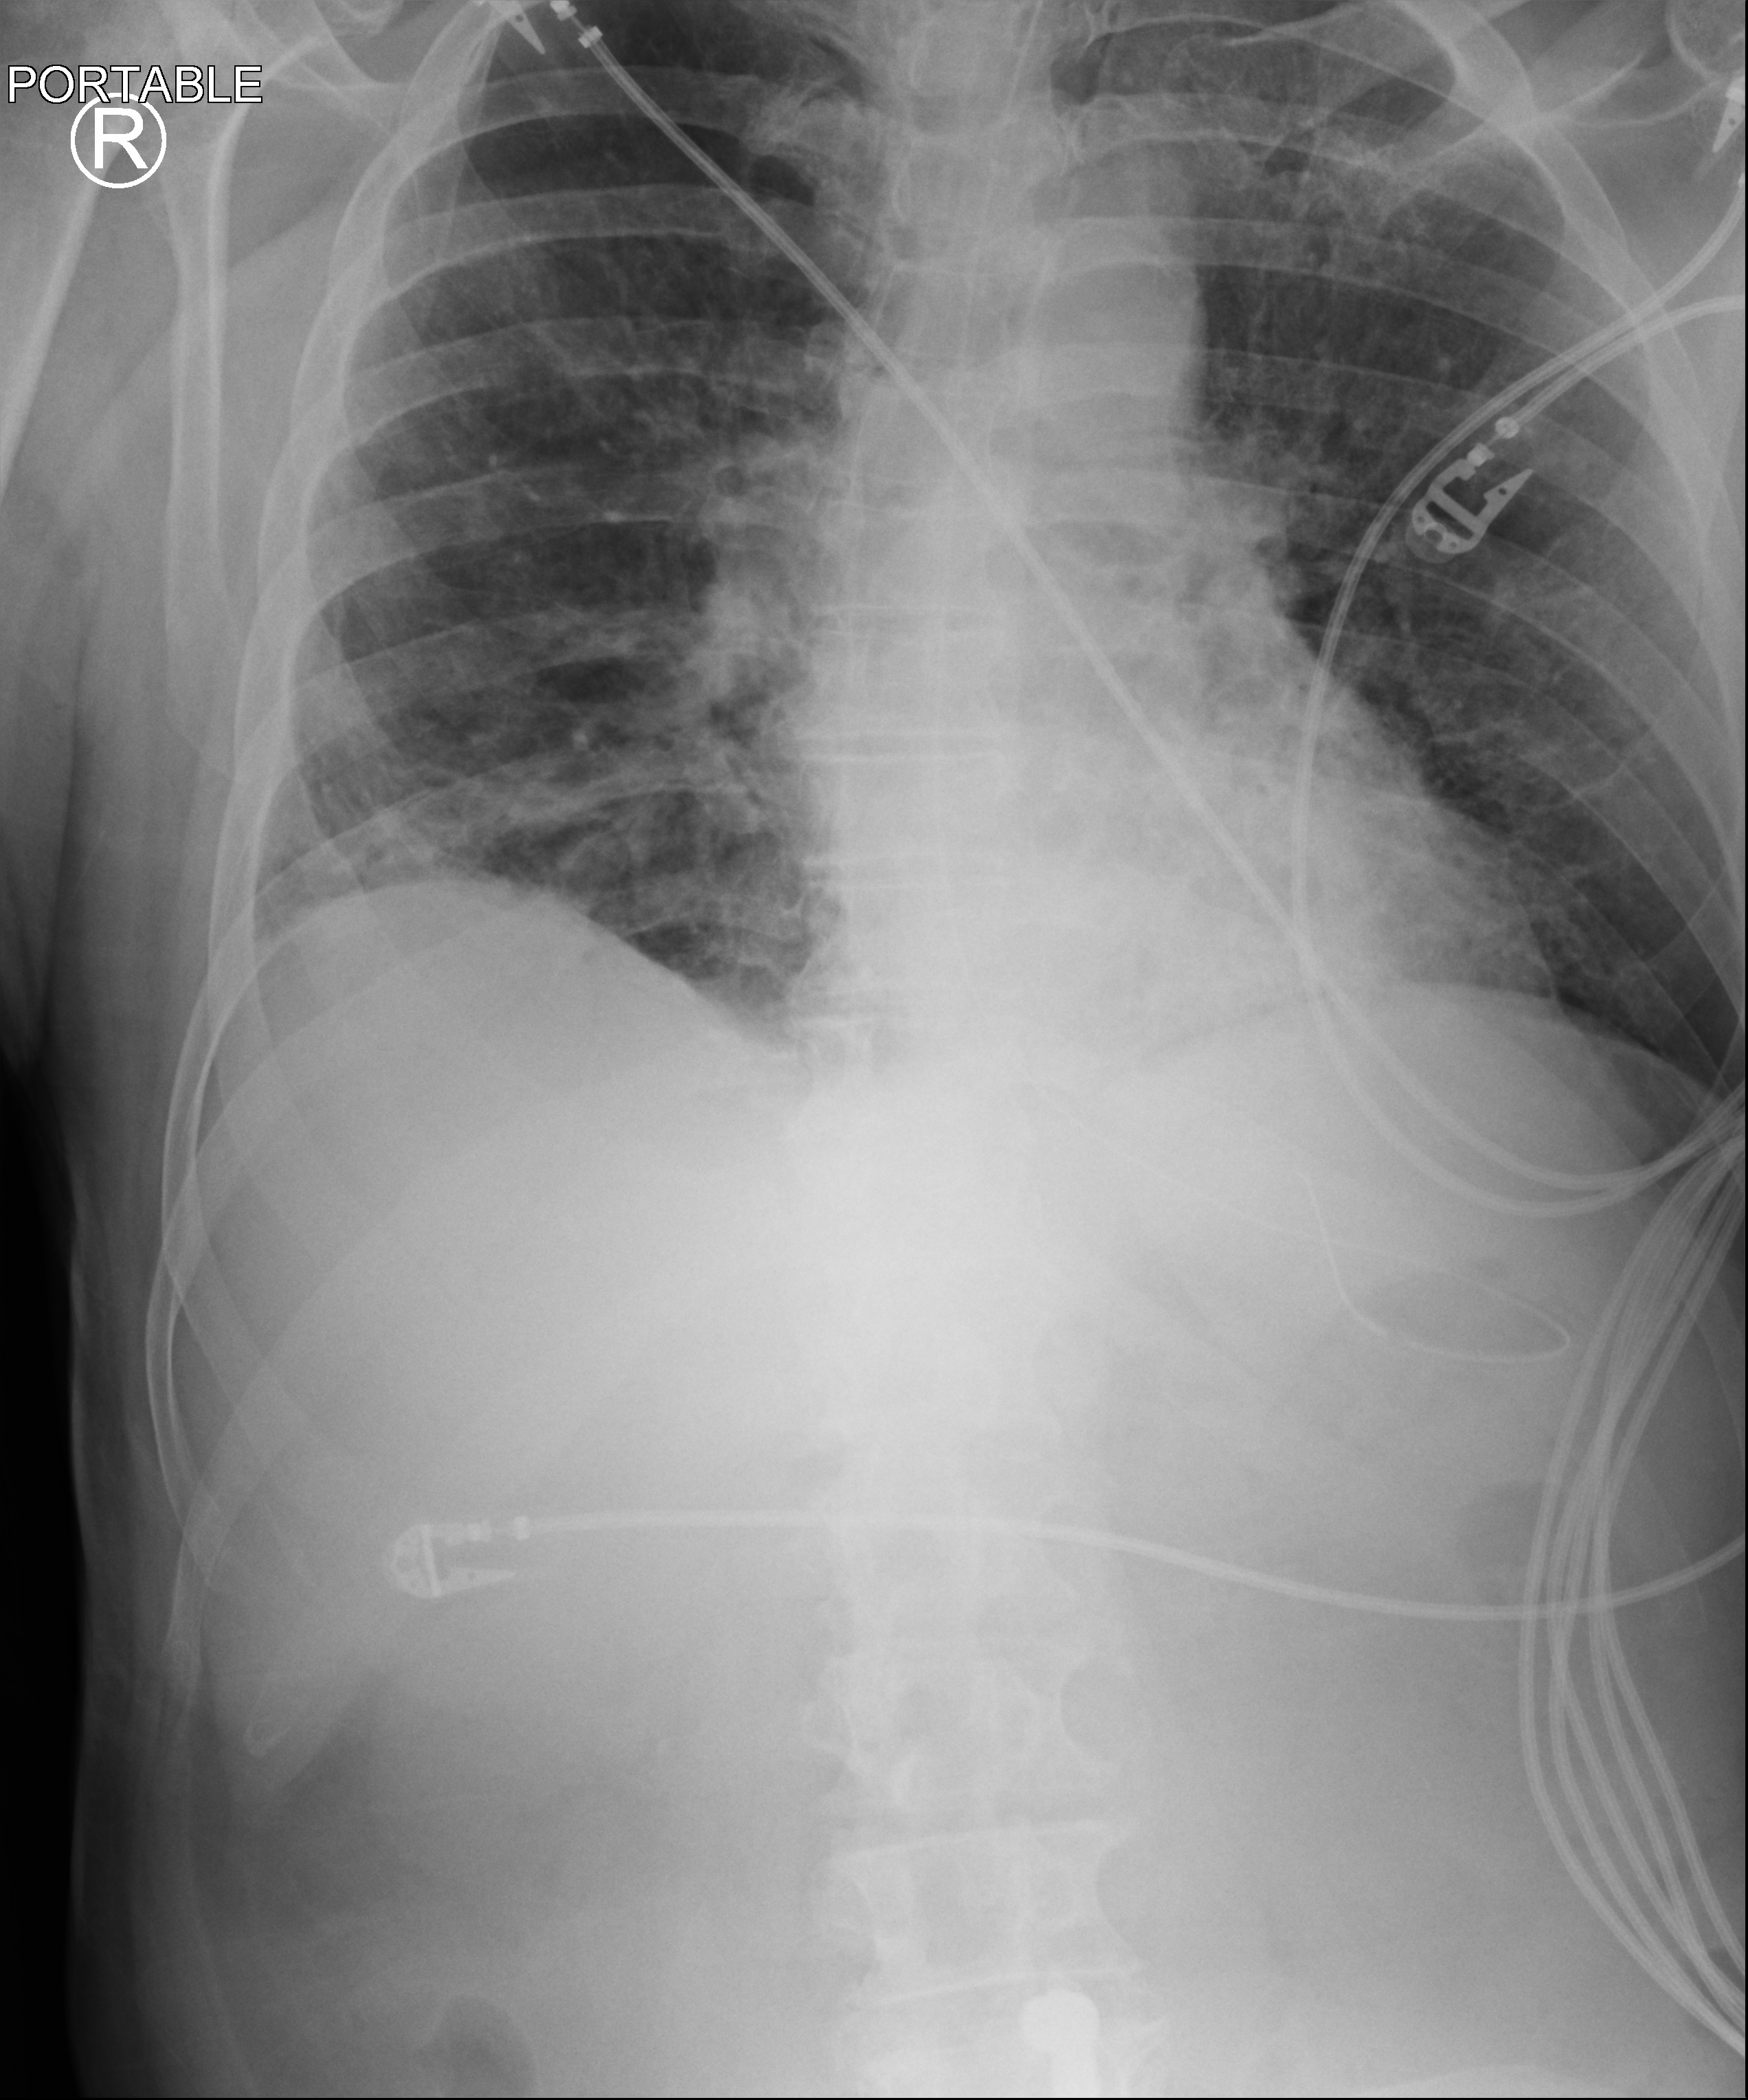
Portable chest radiograph; anteroposterior (AP) projection. Patient hospitalised with COVID-19; male, aged 60–74 years.
Hospital-stay facts (about this admission, not read from this image; timing relative to this image not recorded):
- admitted to intensive care during this hospital stay: yes
- mechanically ventilated during this hospital stay: yes